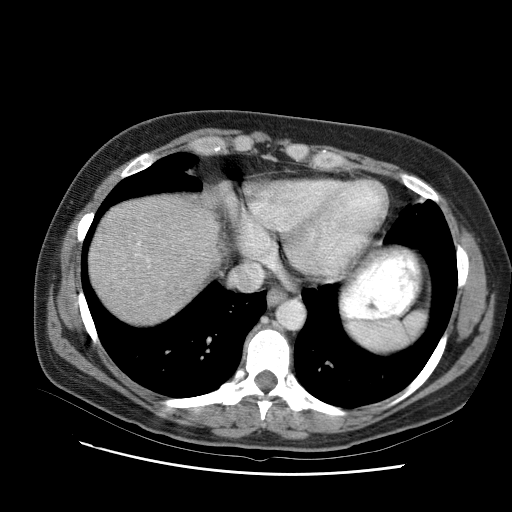
Contrast-enhanced abdominal CT (liver protocol), one axial slice. Position 85 of 95 along the scan axis. Reconstruction kernel STANDARD. 120 kVp. One of 2 acquisitions stored at this slice position. Soft-tissue window (W 400 / L 40 HU). 2.5 mm slice thickness. 512 × 512 image matrix, field of view 360 × 360 mm. Case-level facts recorded for this patient, not image findings: diagnosis: hepatocellular carcinoma (patient treated with transarterial chemoembolisation; whether this scan precedes or follows treatment is not stated here); TNM stage (as recorded): Stage-I.
Outlined on this slice (semi-automatic segmentation, software-assisted and operator-edited):
- liver parenchyma outside the tumour (the mass and vessels are separate outlines, so this box may not span the whole liver): bounding box (x1, y1, x2, y2) in pixels: (100, 206, 204, 296)
- liver vessels: (183, 213, 202, 220)